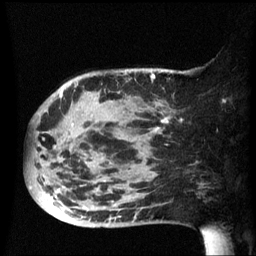
Breast MRI (dynamic contrast-enhanced), one sagittal slice. Dynamic contrast-enhanced series, image 2 of 3 at this slice position (ordered by acquisition). 1.5 T. TE 4.2 ms, TR 8.4 ms. 2.5 mm slice thickness. 256 × 256 image matrix, field of view 220 × 220 mm. Female patient, age 49 years.
Outlined on this slice (semi-automatic segmentation, software-assisted and operator-edited):
- analysis volume of interest (the breast-tissue region the enhancement analysis was run in; not a lesion): box from (x=26, y=72) to (x=185, y=229) px
- tumour enhancement mask (voxels above the 70 % enhancement threshold inside the analysis volume of interest): (x=55, y=74)–(x=171, y=227)